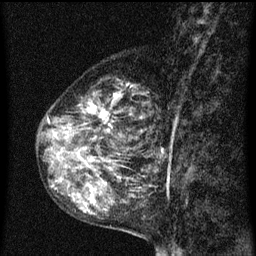
Breast MRI (dynamic contrast-enhanced), one sagittal slice. Position 27 of 60 along the scan axis. Dynamic contrast-enhanced series, image 2 of 3 at this slice position (ordered by acquisition). 1.5 T. TE 4.2 ms, TR 8 ms. 2 mm slice thickness. 256 × 256 image matrix, field of view 180 × 180 mm. Patient: female, 55 years.
Outlined on this slice (semi-automatically segmented with operator editing):
- analysis volume of interest (the breast-tissue region the enhancement analysis was run in; not a lesion): box from (x=38, y=80) to (x=159, y=151) px
- tumour enhancement mask (voxels above the 70 % enhancement threshold inside the analysis volume of interest): (x=48, y=84)–(x=131, y=141)